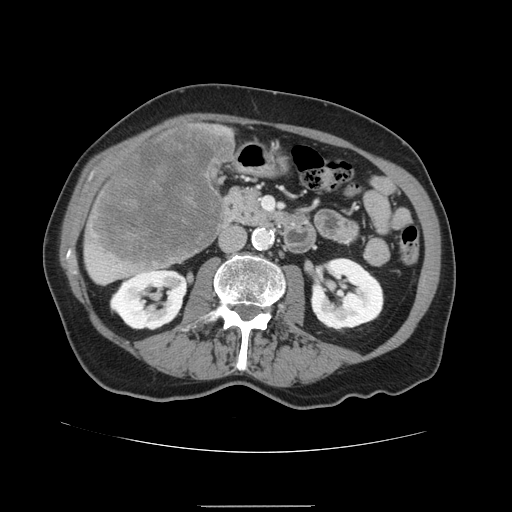
Contrast-enhanced abdominal CT, one axial slice. Slice 48 of 168 in the series (ordered by position). Soft-tissue window (W 400 / L 40 HU). 512 × 512 image matrix, field of view 386 × 386 mm. Male patient, age 74 years. From the clinical record (not read from this slice): diagnosis: colorectal cancer liver metastases, imaged before liver resection; multiple liver metastases: no; largest metastasis: 14.5 cm.
Annotated regions visible in this slice (outlined manually by an expert reader):
- liver: bounding box [x1, y1, x2, y2] px = [83, 121, 236, 285]
- liver metastasis: [91, 126, 233, 267]